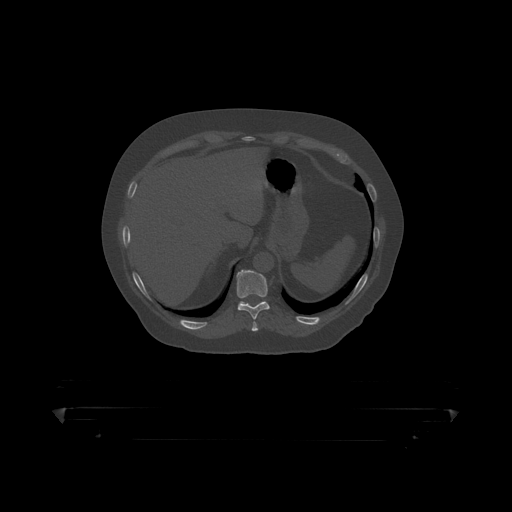
CT including the spine, one axial slice. Position 214 of 390 along the scan axis. Reconstruction kernel STANDARD. 120 kVp. Bone window (W 1800 / L 400 HU). 1.25 mm slice thickness. 512 × 512 image matrix, field of view 650 × 650 mm. Patient: male, 60 years. Case-level facts recorded for this patient, not image findings: primary cancer: prostate.
Structures marked on this image (semi-automatically segmented with operator editing):
- T10 vertebra: bounding box <237,270,270,319> (left, top, right, bottom; pixels)
- T11 vertebra: <241,302,245,304>